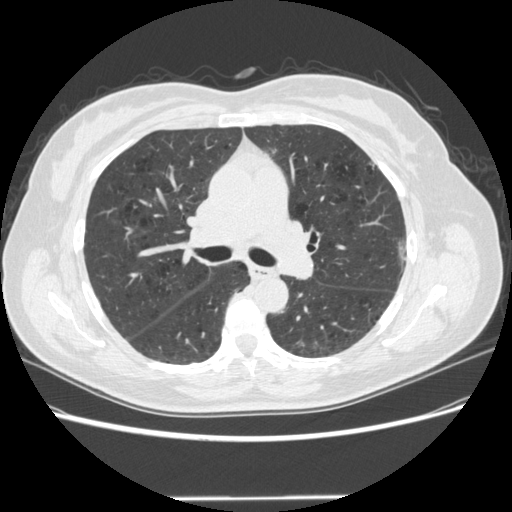
Low-dose screening chest CT, axial slice. Baseline screening round. Lung window (W 1500 / L -600 HU). 1.25 mm slice thickness. Female participant, aged 61 years at enrolment. Current smoker at enrolment.
- Expert-annotated lung lesion, bounding box [x1, y1, x2, y2] px = [382, 226, 425, 277].
- No non-calcified nodule or mass ≥4 mm was recorded by the screening reader at this exam.